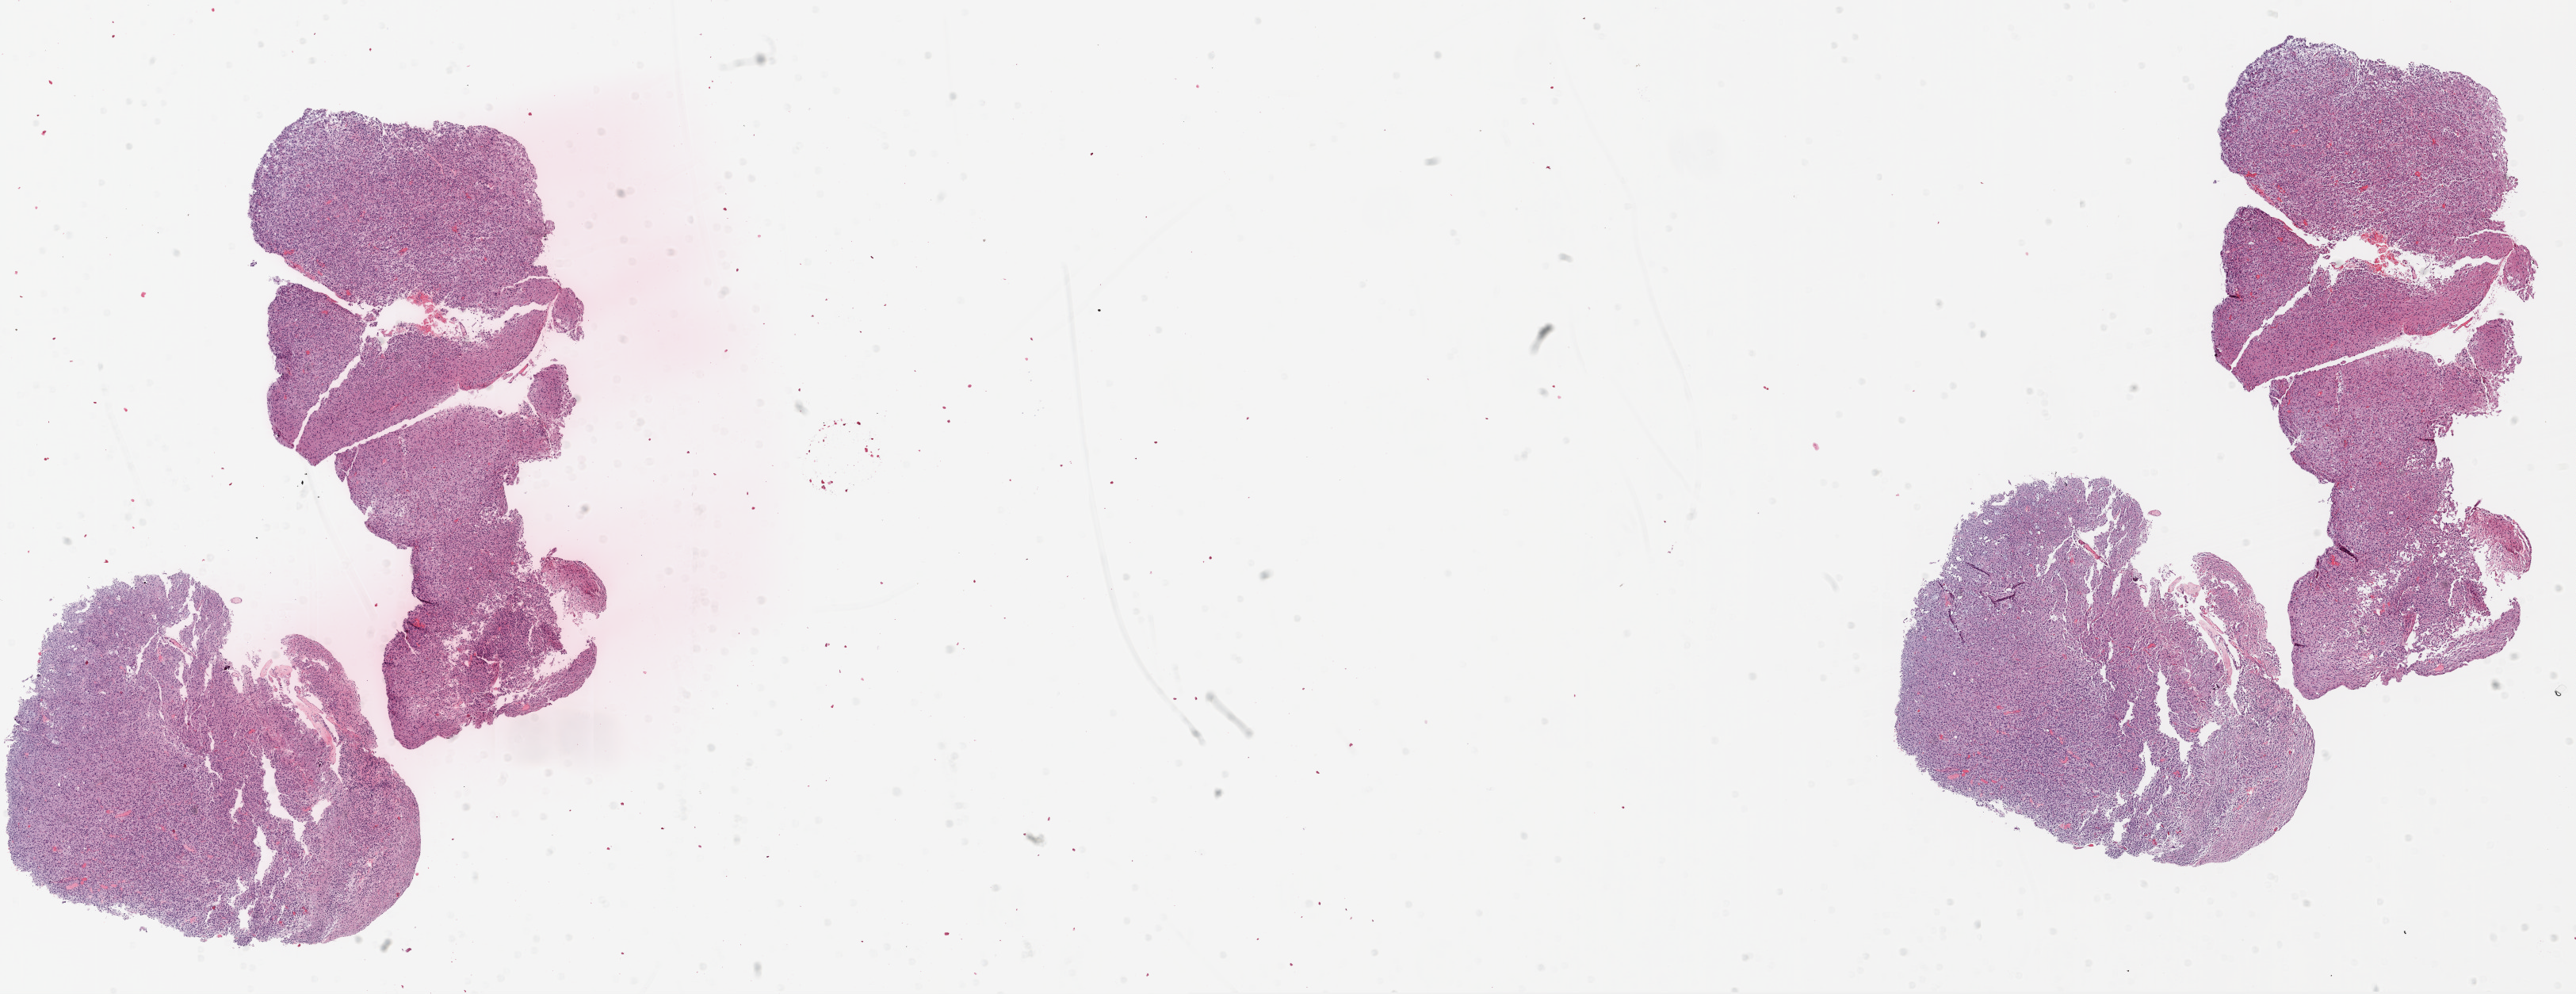
Digitized Hematoxylin and eosin (H&E) stained tissue section (whole slide) — whole scanned area (about 26.1 x 10.1 mm, slide scanned at 20x) shown as a low-resolution overview, FFPE section, primary tumour sample from the brain. Male patient; age at initial diagnosis 54 years.
Histologic diagnosis: Glioblastoma.